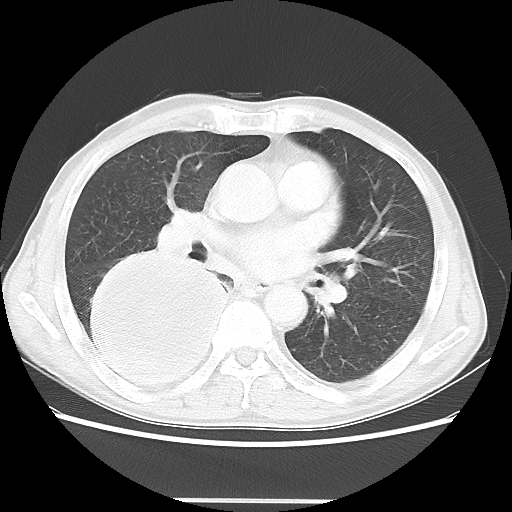
Chest CT, one axial slice; slice 24 of 48 in the series (ordered by position); reconstruction kernel LUNG; 100 kVp; lung window (W 1500 / L -600 HU); 512 × 512 image matrix, field of view 361 × 361 mm. Male patient, age 66 years. Case-level facts recorded for this patient, not image findings: clinical TNM (as recorded): T4 N1 M1; histopathological grade: G3.
Structures marked on this image (bounding box drawn by a radiologist):
- lung tumour (recorded histology: small cell carcinoma): bounding box (x1, y1, x2, y2) in pixels: (66, 246, 239, 398)